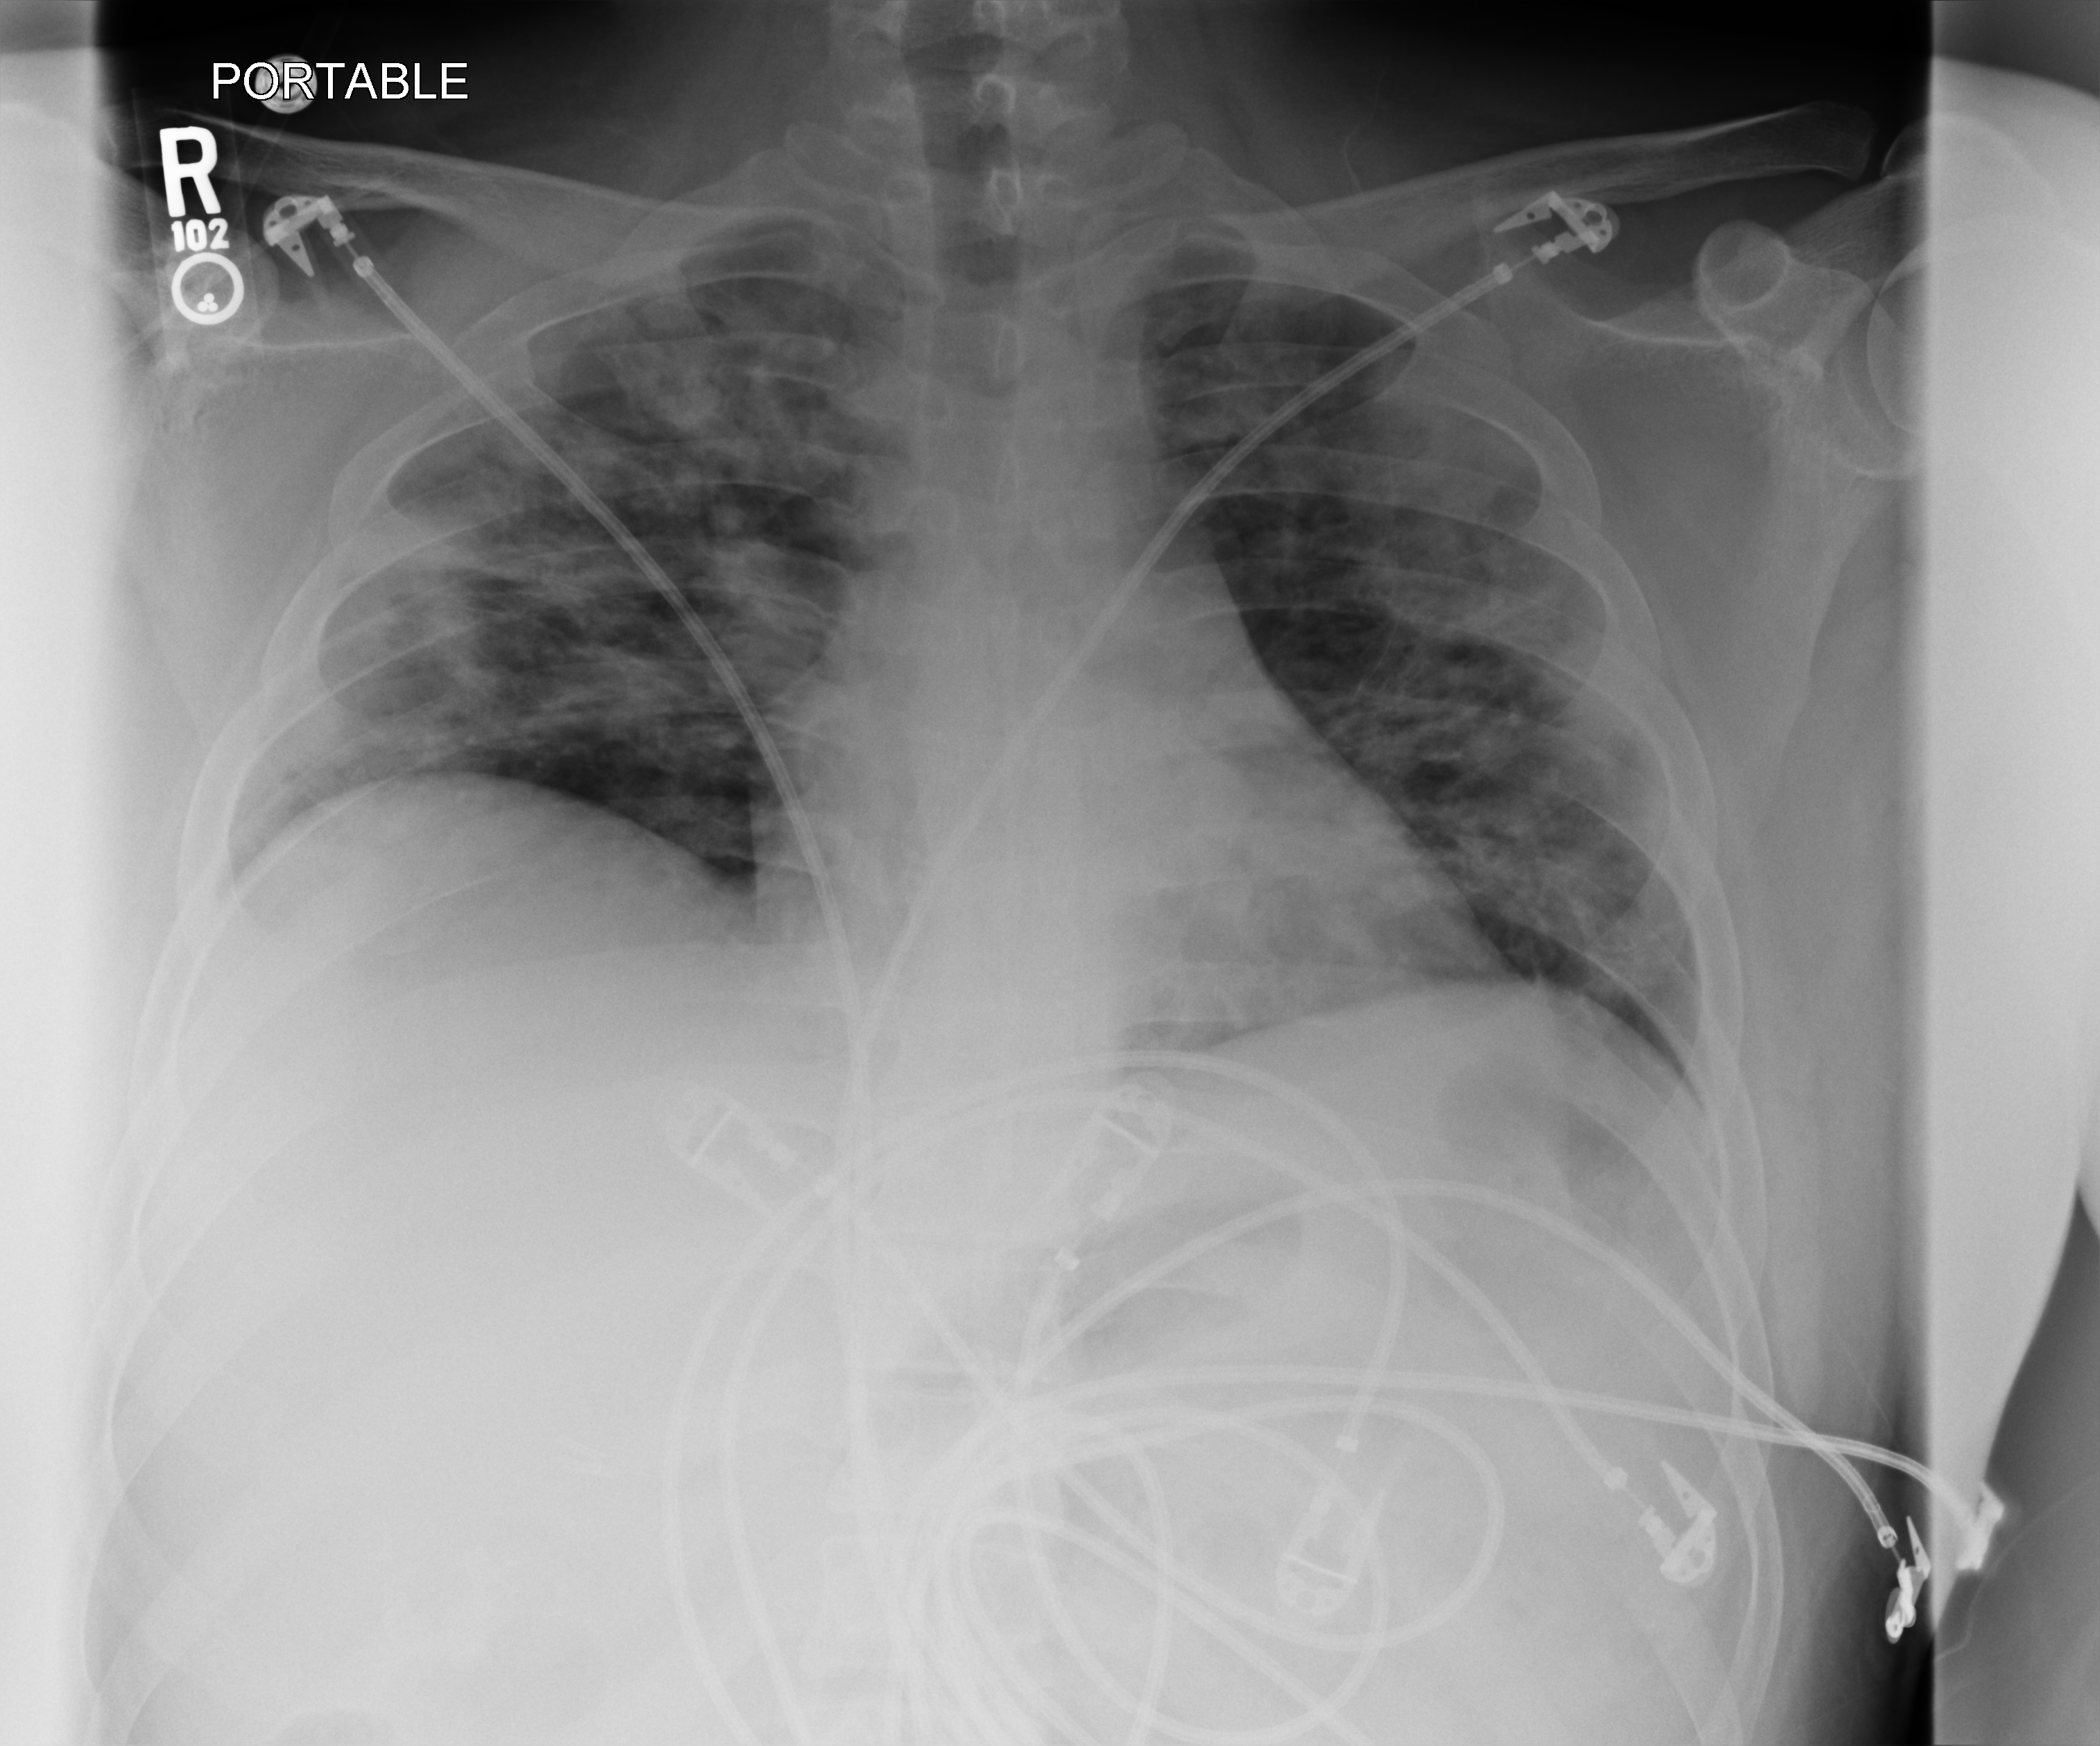
Bedside chest radiograph (computed radiography), anteroposterior (AP) projection. Patient hospitalised with COVID-19; male, aged 18–59 years.
Hospital-stay facts (about this admission, not read from this image; timing relative to this image not recorded):
- length of hospital stay: 44 days
- diabetes (admission record): yes
- mechanically ventilated during this hospital stay: yes